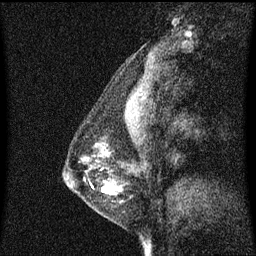
Breast MRI (dynamic contrast-enhanced), one sagittal slice. Position 19 of 60 along the scan axis. Dynamic contrast-enhanced series, image 2 of 3 at this slice position (ordered by acquisition). 1.5 T. TE 4.2 ms, TR 8.4 ms. 2 mm slice thickness. 256 × 256 image matrix, field of view 200 × 200 mm. Female patient, age 41 years. Case-level facts recorded for this patient, not image findings: setting: breast cancer imaged before/during neoadjuvant chemotherapy; receptor status: triple-negative.
Annotated regions visible in this slice (semi-automatic segmentation, software-assisted and operator-edited):
- analysis volume of interest (the breast-tissue region the enhancement analysis was run in; not a lesion): bounding box (x1, y1, x2, y2) in pixels: (64, 144, 135, 209)
- tumour enhancement mask (voxels above the 70 % enhancement threshold inside the analysis volume of interest): (102, 188, 117, 193)